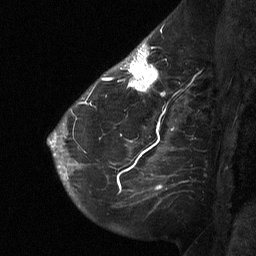
Breast MRI (dynamic contrast-enhanced), one sagittal slice. Slice 42 of 64 in the series (ordered by position). Dynamic contrast-enhanced study with each time point stored as its own series, time point 2 of 3 at this slice position (early post-contrast, ordered by acquisition time). 1.5 T. TE 4.8 ms, TR 27 ms. 2 mm slice thickness. 256 × 256 image matrix, field of view 200 × 200 mm. Female patient, age 51 years. From the clinical record (not read from this slice): setting: breast cancer imaged before/during neoadjuvant chemotherapy; receptor status: HR-positive, HER2-negative.
Annotated regions visible in this slice (semi-automatic segmentation, software-assisted and operator-edited):
- analysis volume of interest (the breast-tissue region the enhancement analysis was run in; not a lesion): bounding box <112,46,167,97> (left, top, right, bottom; pixels)
- tumour enhancement mask (voxels above the 90 % enhancement threshold inside the analysis volume of interest): <112,46,159,92>